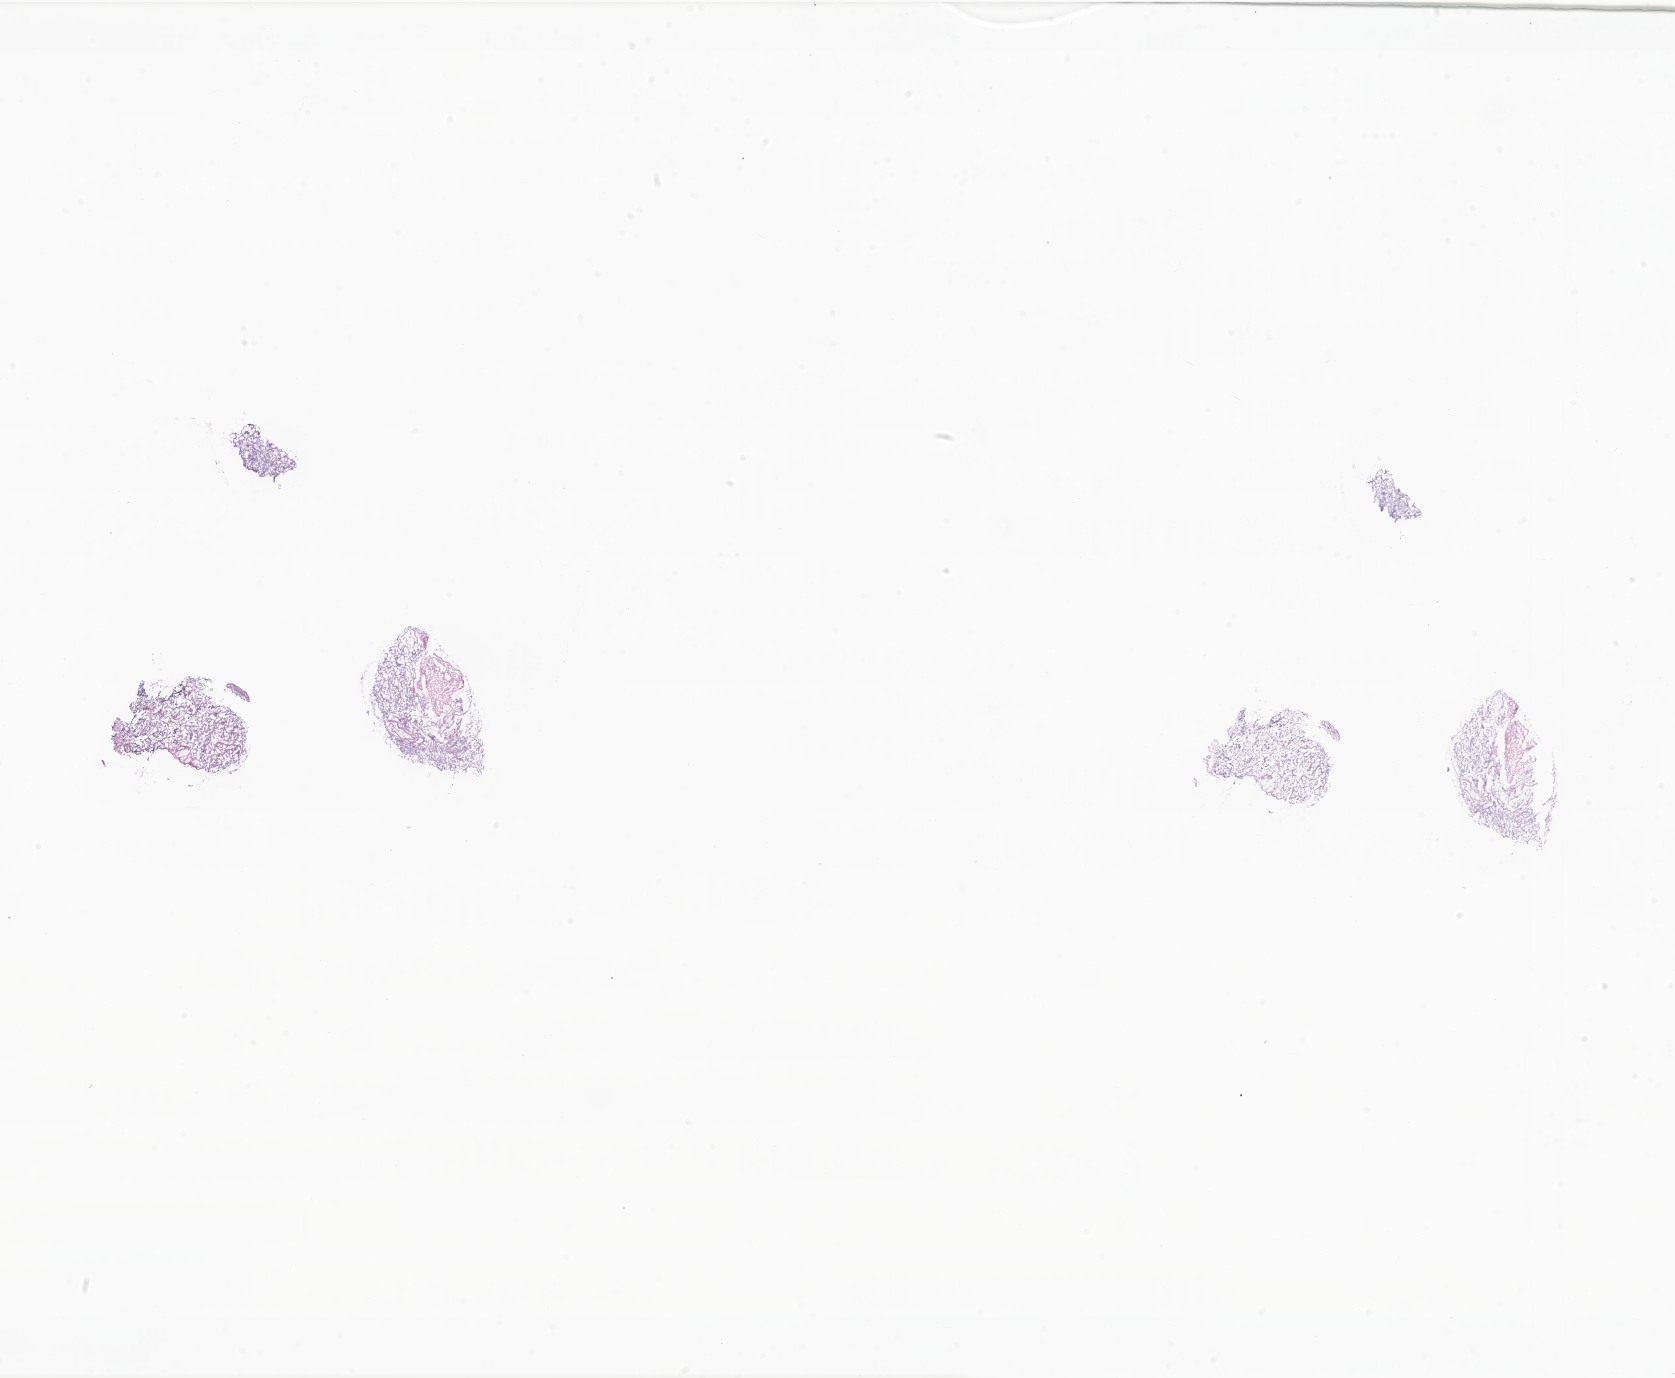
Digitized H&E-stained section, whole scanned area (about 28.2 x 23.2 mm) shown as a low-resolution overview. Frozen section. Specimen: primary tumor. Anatomic site: upper lobe of left lung. Female, age 66 years at initial diagnosis. Tumor grade: G3 (poorly differentiated). Composition of this section per pathologist review: tumor cells 80%, tumor nuclei 80%, stromal cells 18%, necrosis 0%, normal cells 2%. Inflammatory infiltration, as recorded: lymphocyte infiltration 5%, monocyte infiltration 4%, neutrophil infiltration 4%.
AJCC pathologic stage: Stage IB. Section: bottom of the tissue portion. Histologic diagnosis: Adenocarcinoma, NOS.